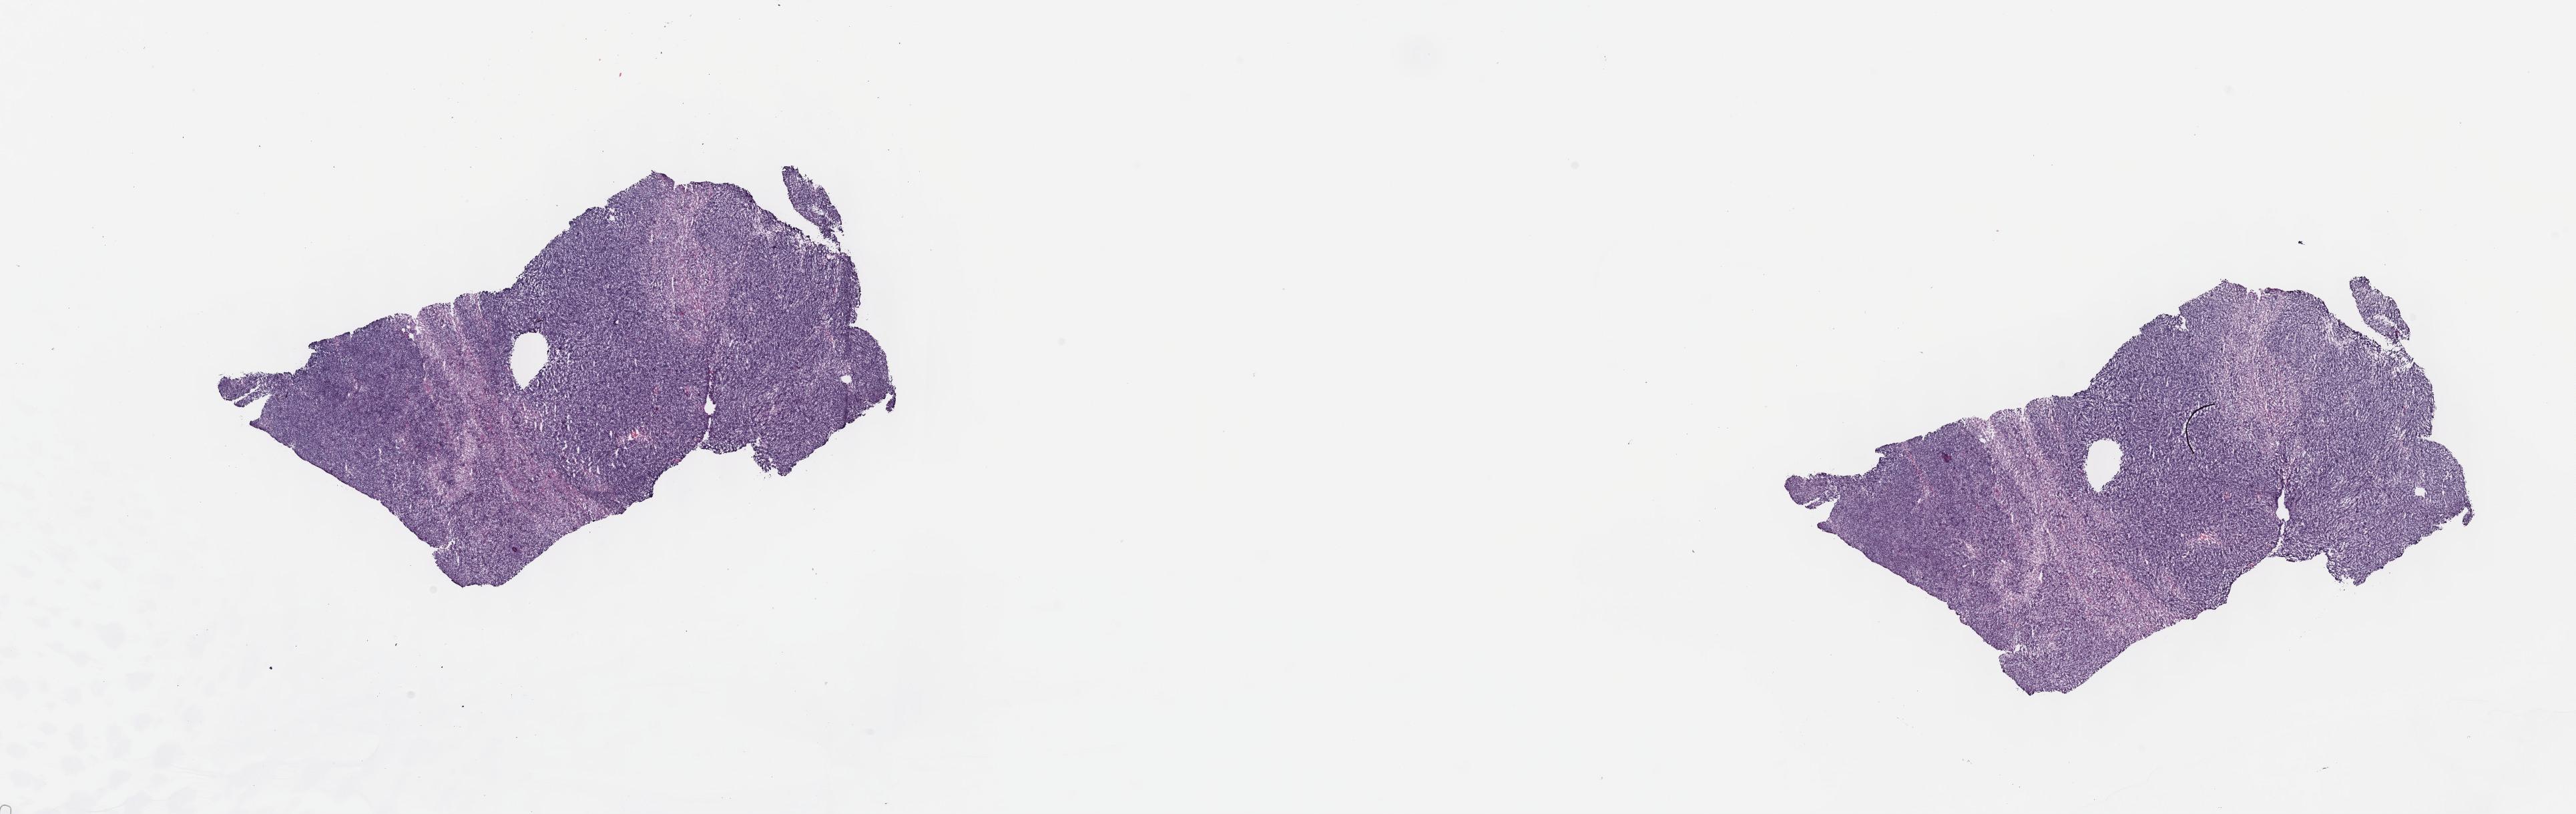
Digitized H&E tissue section (whole slide), a low-resolution overview of the entire scanned area, about 31.2 x 9.9 mm (slide scanned at 40x), frozen section from the top of the tissue portion, thymus, primary tumour sample. Male, age 67 years at initial diagnosis. Composition of this section per pathologist review: tumour cells 90%, tumour nuclei 95%.
Diagnosis: Thymoma, type AB, NOS.